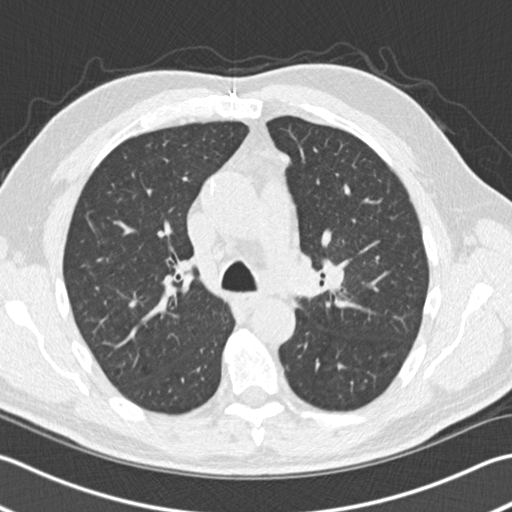
Low-dose screening chest CT, one axial slice; position 101 of 153 along the scan axis; 120 kVp; lung window (W 1500 / L -600 HU); 512 × 512 image matrix, field of view 346 × 346 mm.
Structures marked on this image (outlined manually by an expert reader):
- lesion 1 (tumor, upper lobe of left lung): bounding box [x1, y1, x2, y2] px = [325, 266, 345, 288]